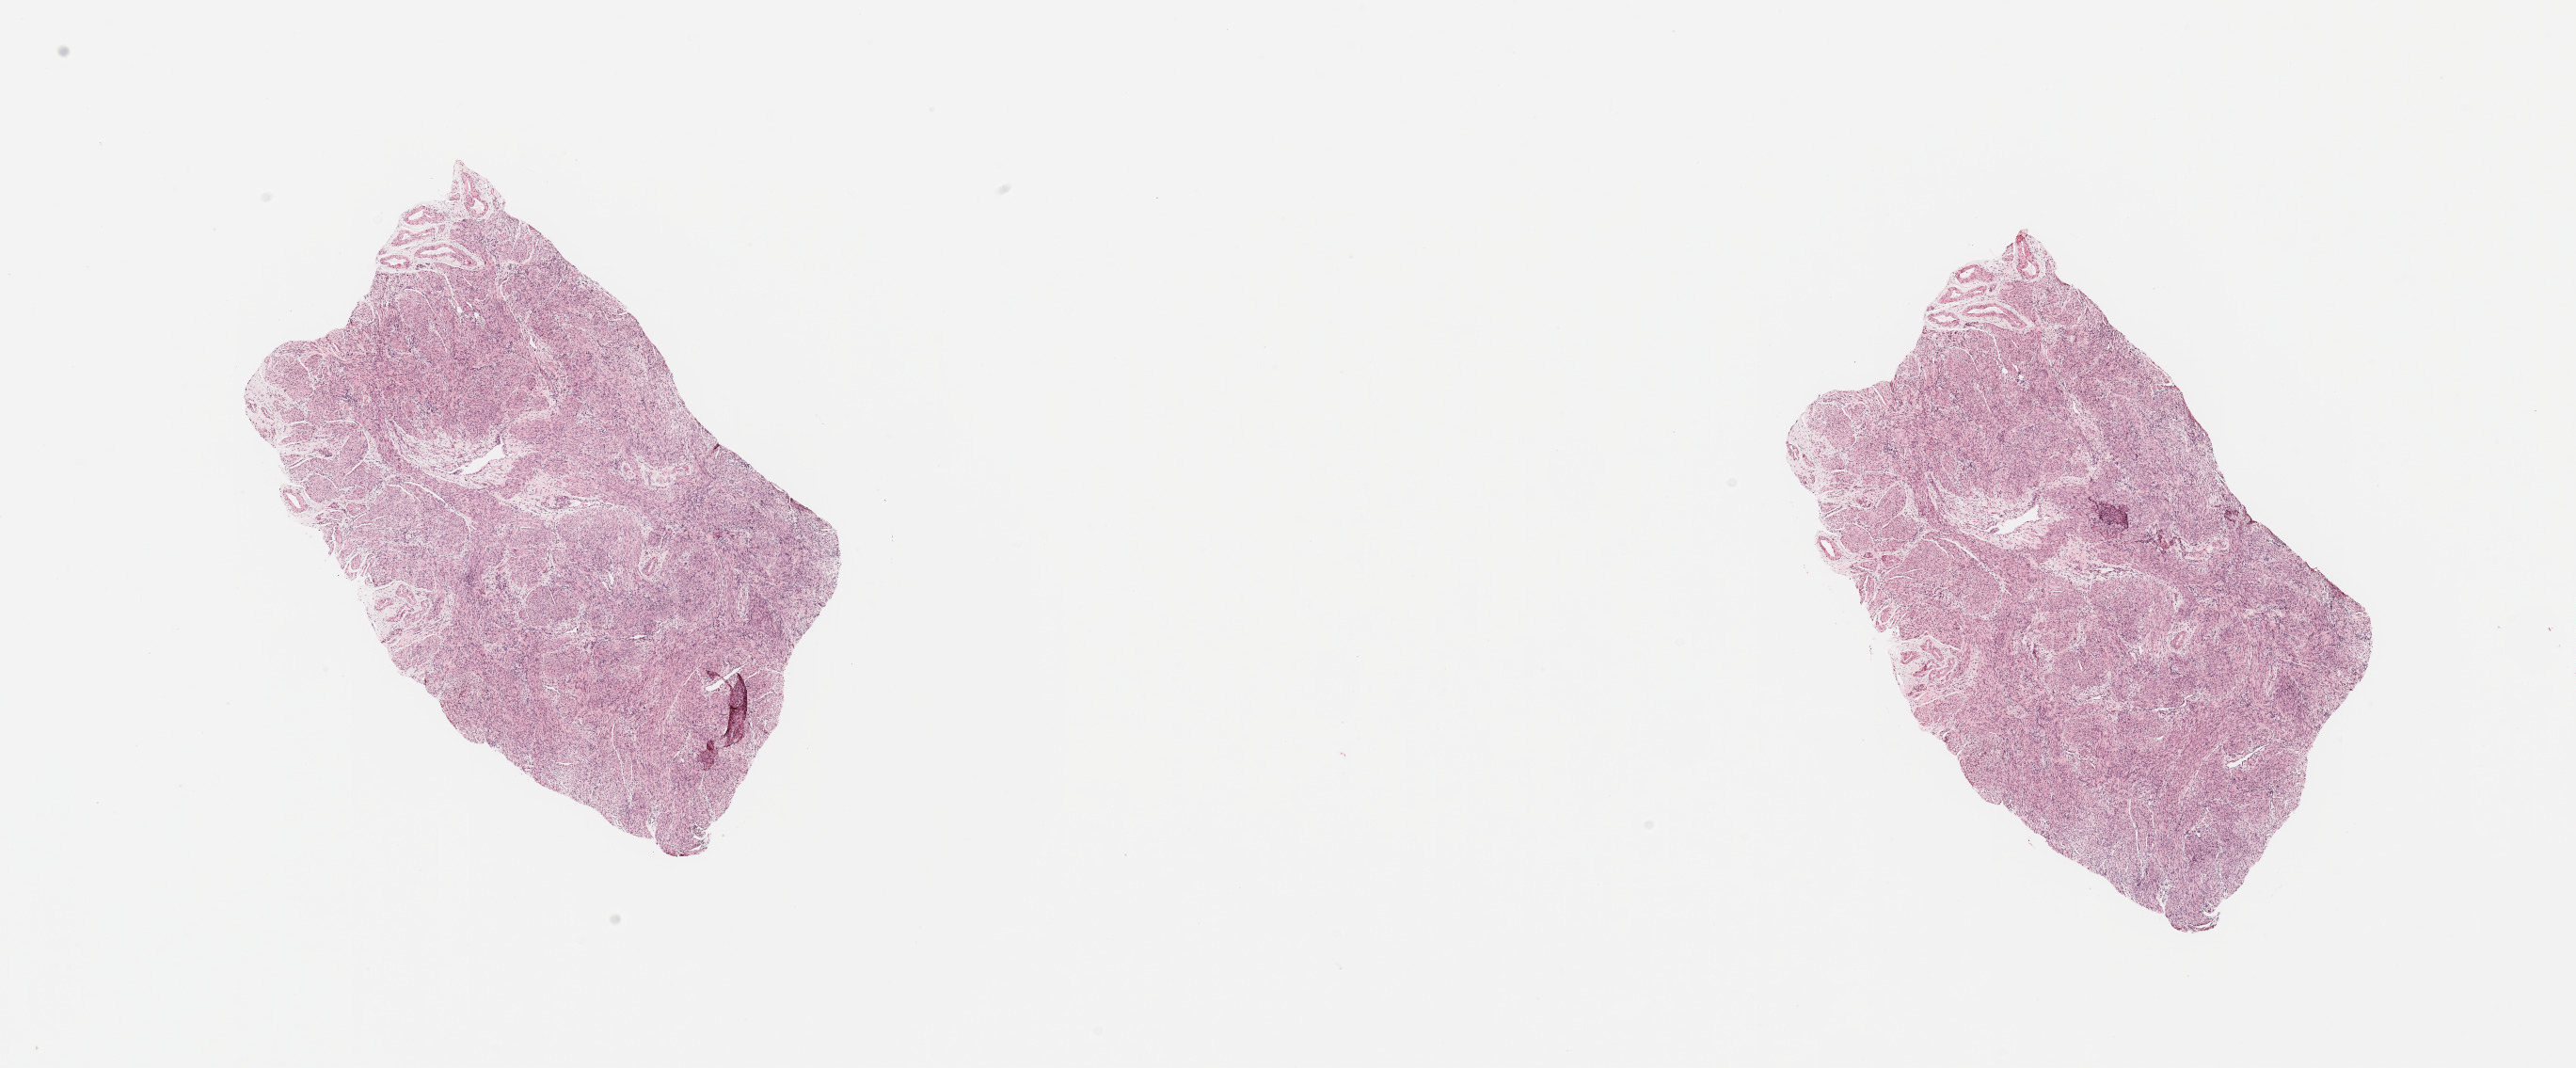
Whole-slide histology image, Hematoxylin and eosin (H&E) stained — shown as a low-resolution overview of the whole scanned area (about 21.7 x 9.0 mm), uterus, normal (non-tumour) tissue. 81-year-old female patient.
• this section: normal (non-tumour) tissue from the same patient
• patient diagnosis (cohort enrolment): corpus endometrial carcinoma (uterus)